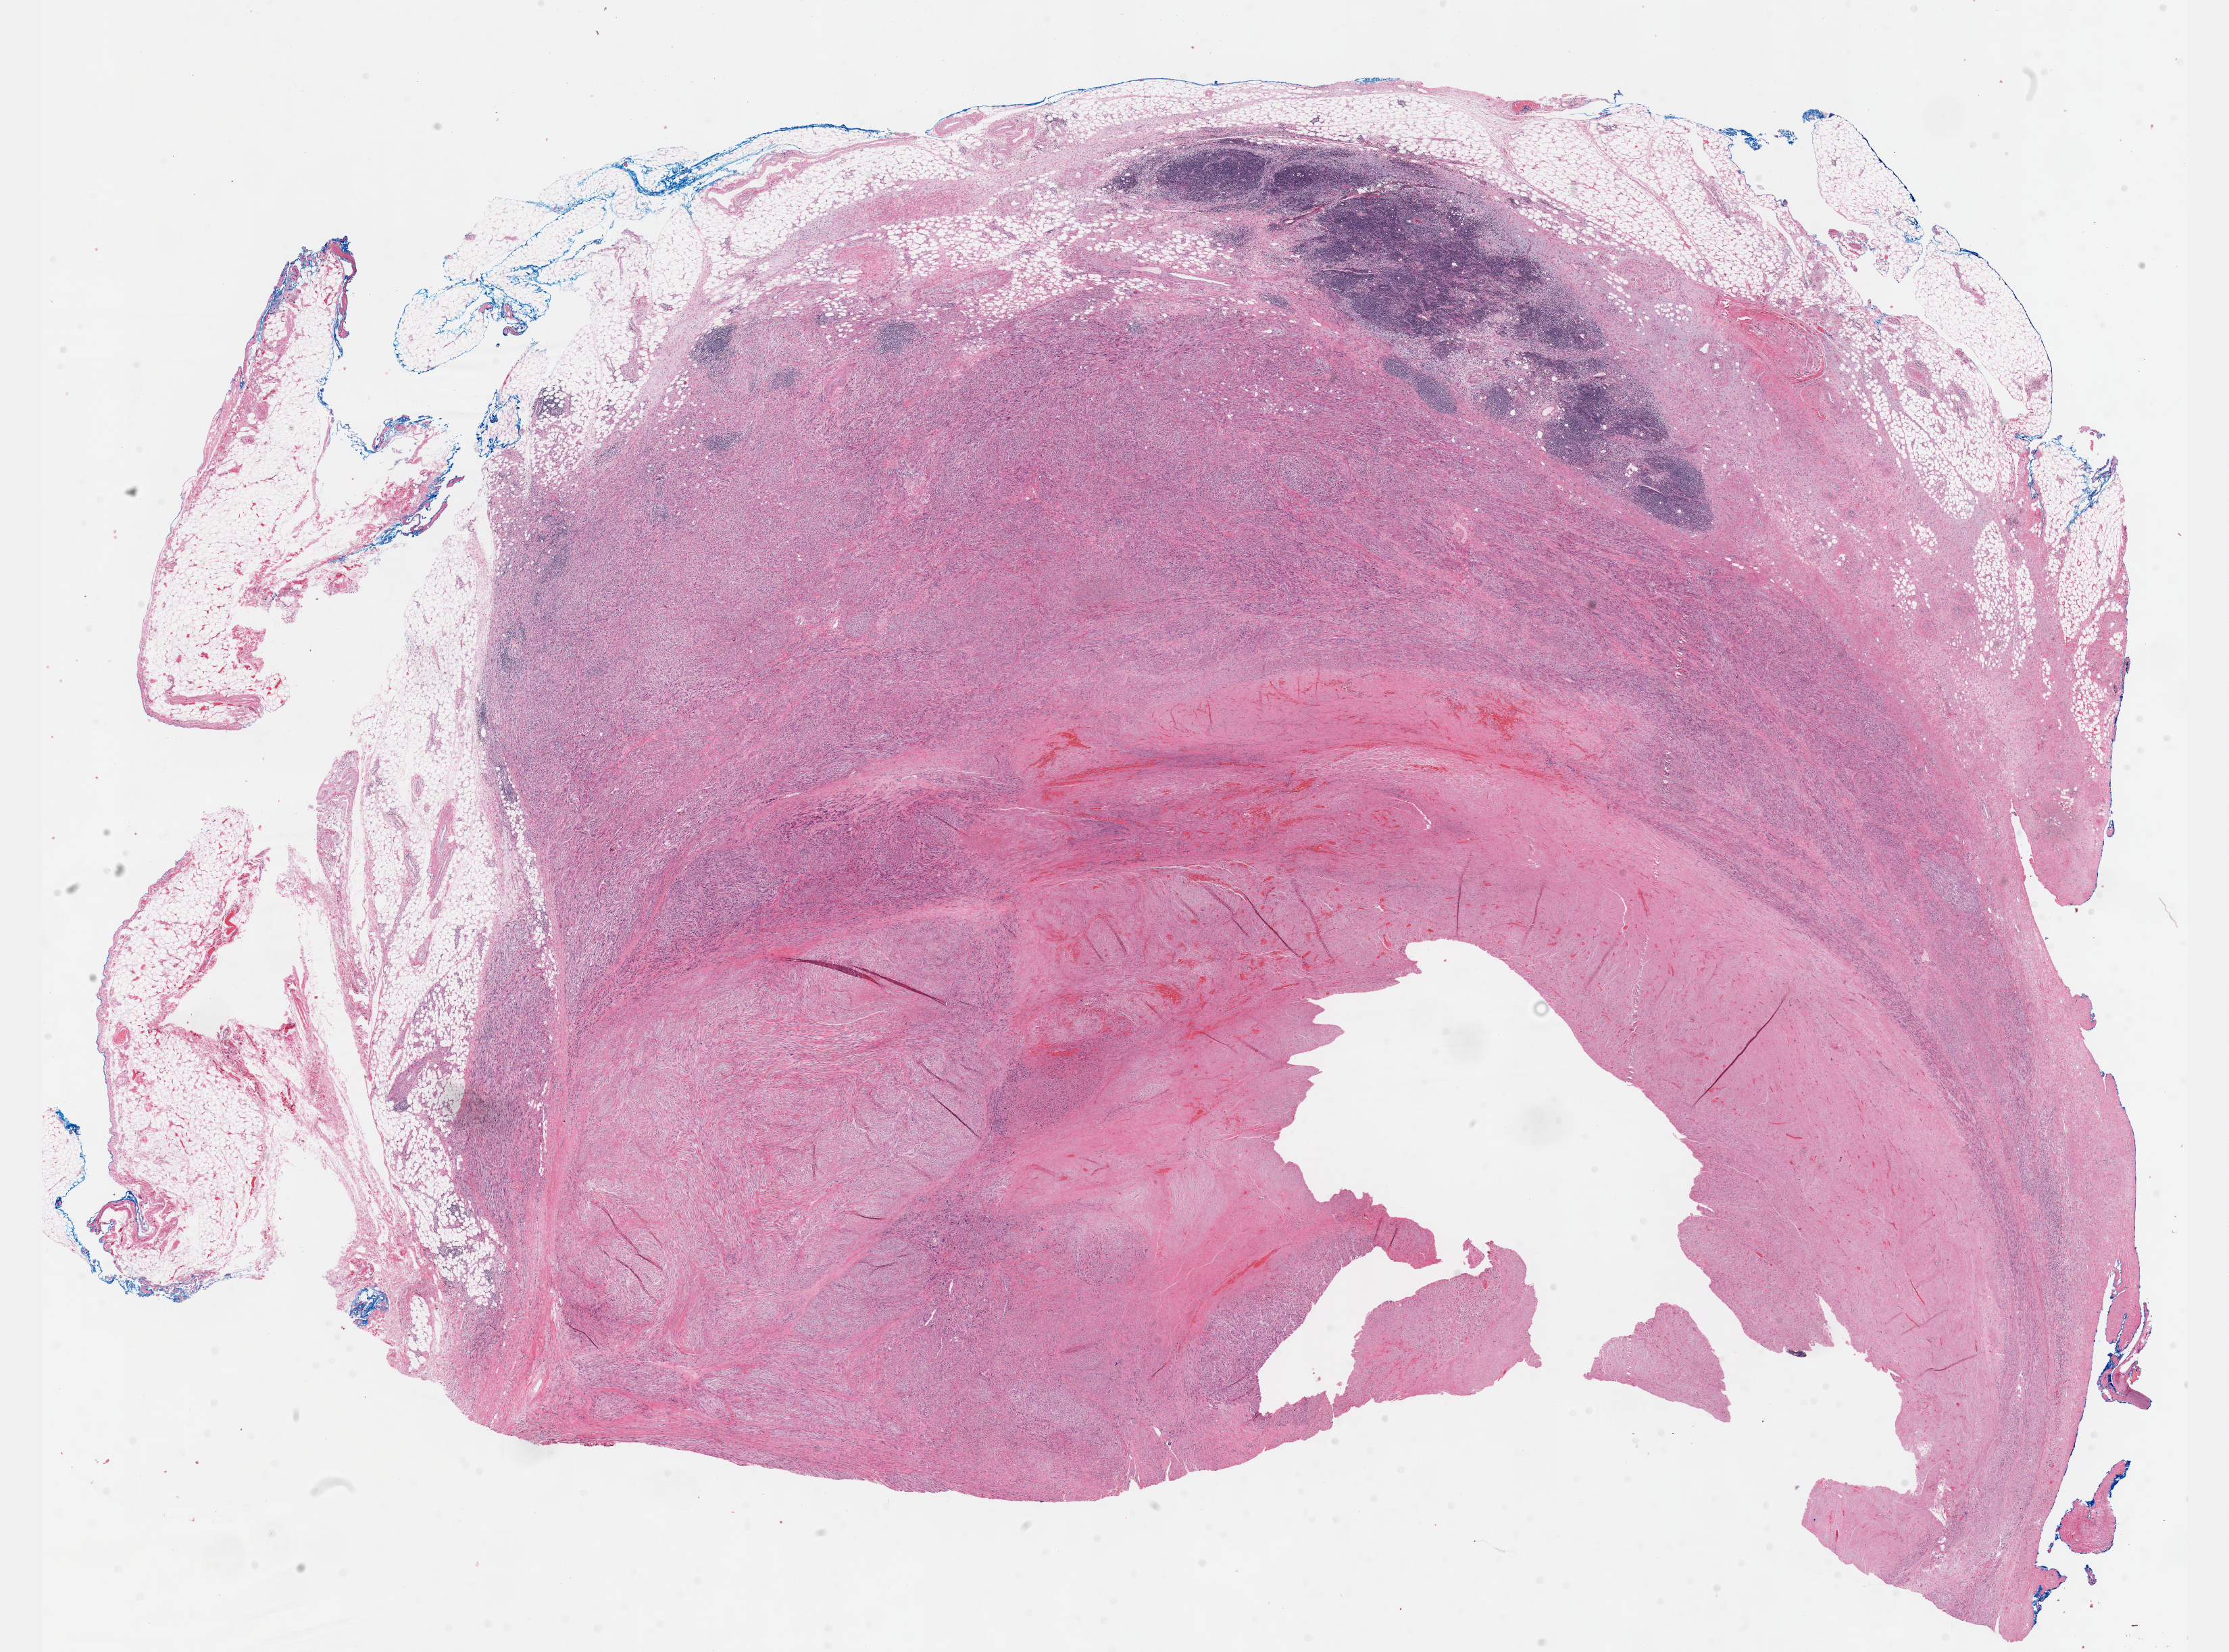
H&E-stained whole-slide image — shown as a low-resolution overview of the whole scanned area (about 26.7 x 19.8 mm); formalin-fixed paraffin-embedded (FFPE) diagnostic section; primary tumour sample from the connective, subcutaneous and other soft tissues. Patient sex: female.
- pathologic diagnosis: Leiomyosarcoma, NOS (connective, subcutaneous and other soft tissues of thorax)